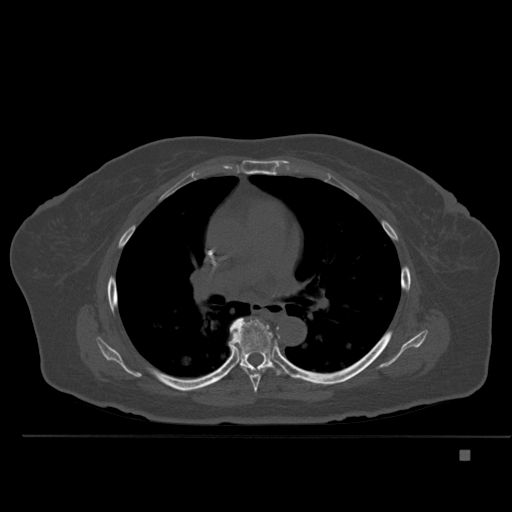
CT including the spine, one axial slice; position 332 of 477 along the scan axis; bone window (W 1800 / L 400 HU); 1.5 mm slice thickness; 512 × 512 image matrix, field of view 422 × 422 mm. Female patient, age 74 years. From the clinical record (not read from this slice): primary cancer: colon.
Annotated regions visible in this slice (semi-automatically segmented with operator editing):
- T6 vertebra: box from (x=241, y=367) to (x=268, y=393) px
- T7 vertebra: (x=229, y=318)–(x=287, y=376)